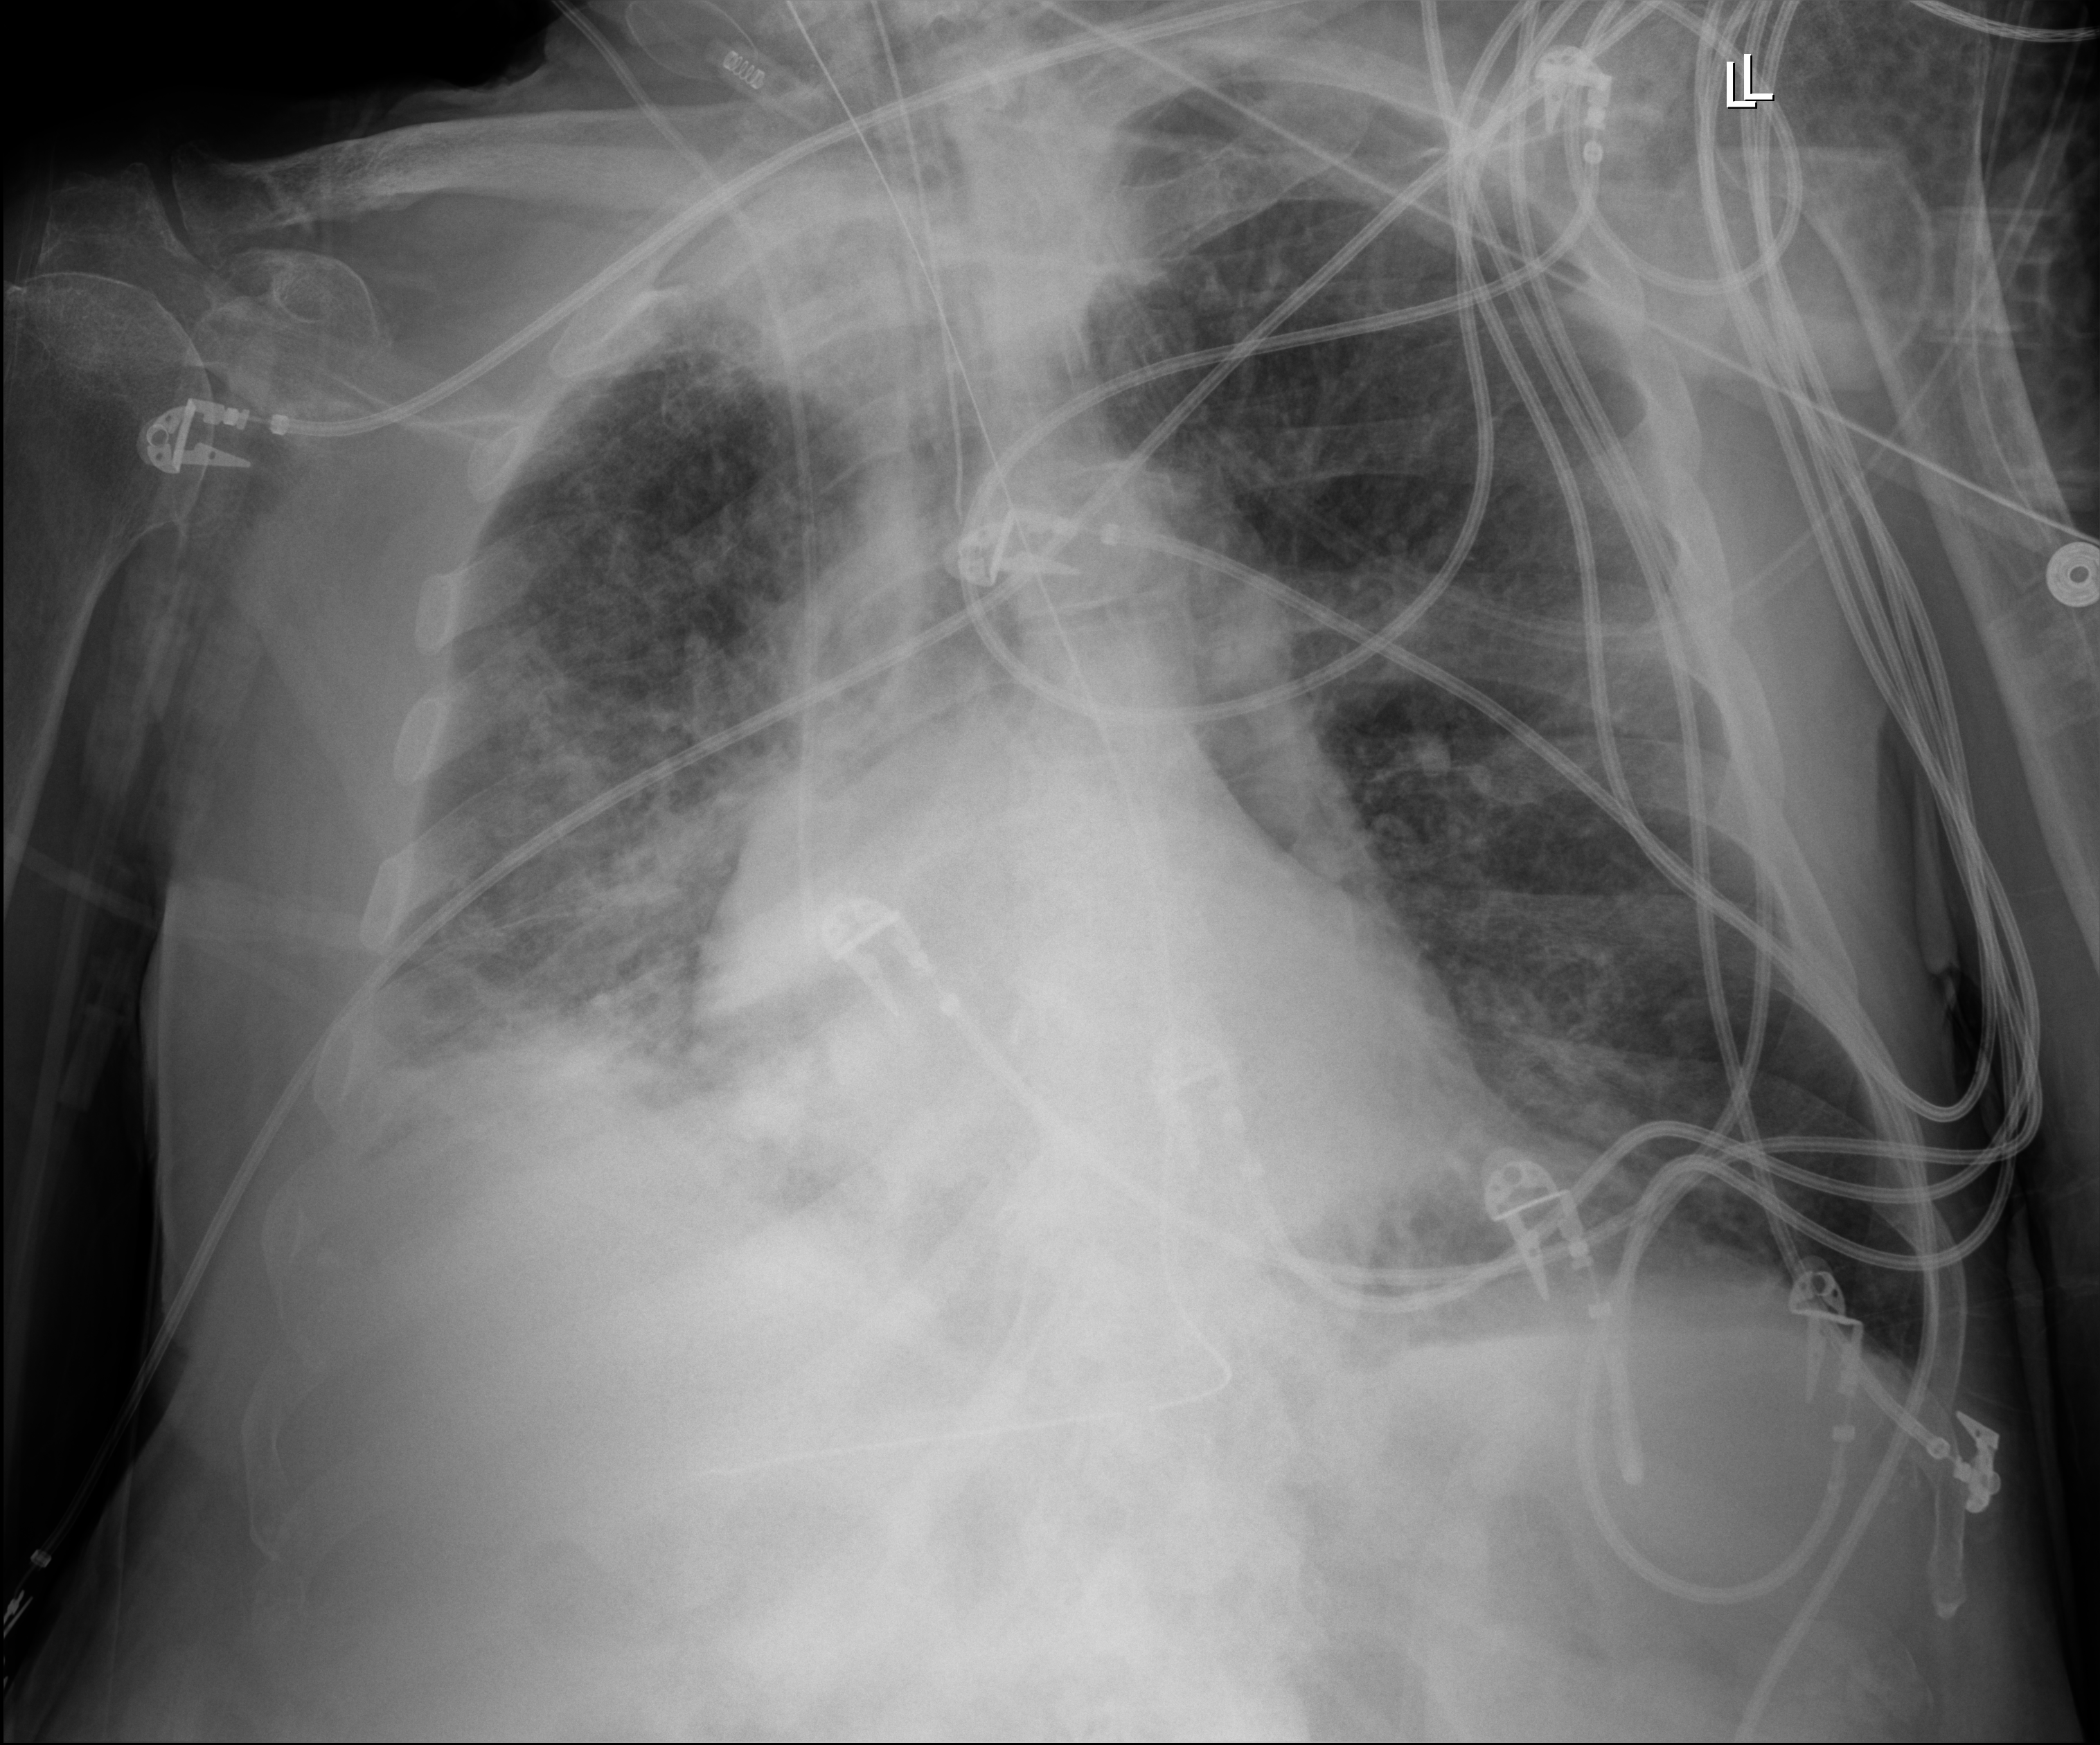
Portable chest radiograph. Patient hospitalised with COVID-19; male, aged 75–90 years.
Admission-level facts for this patient (not findings on this image; timing relative to this image not recorded):
- COPD (admission record): no
- admitted to intensive care during this hospital stay: yes
- mechanically ventilated during this hospital stay: yes